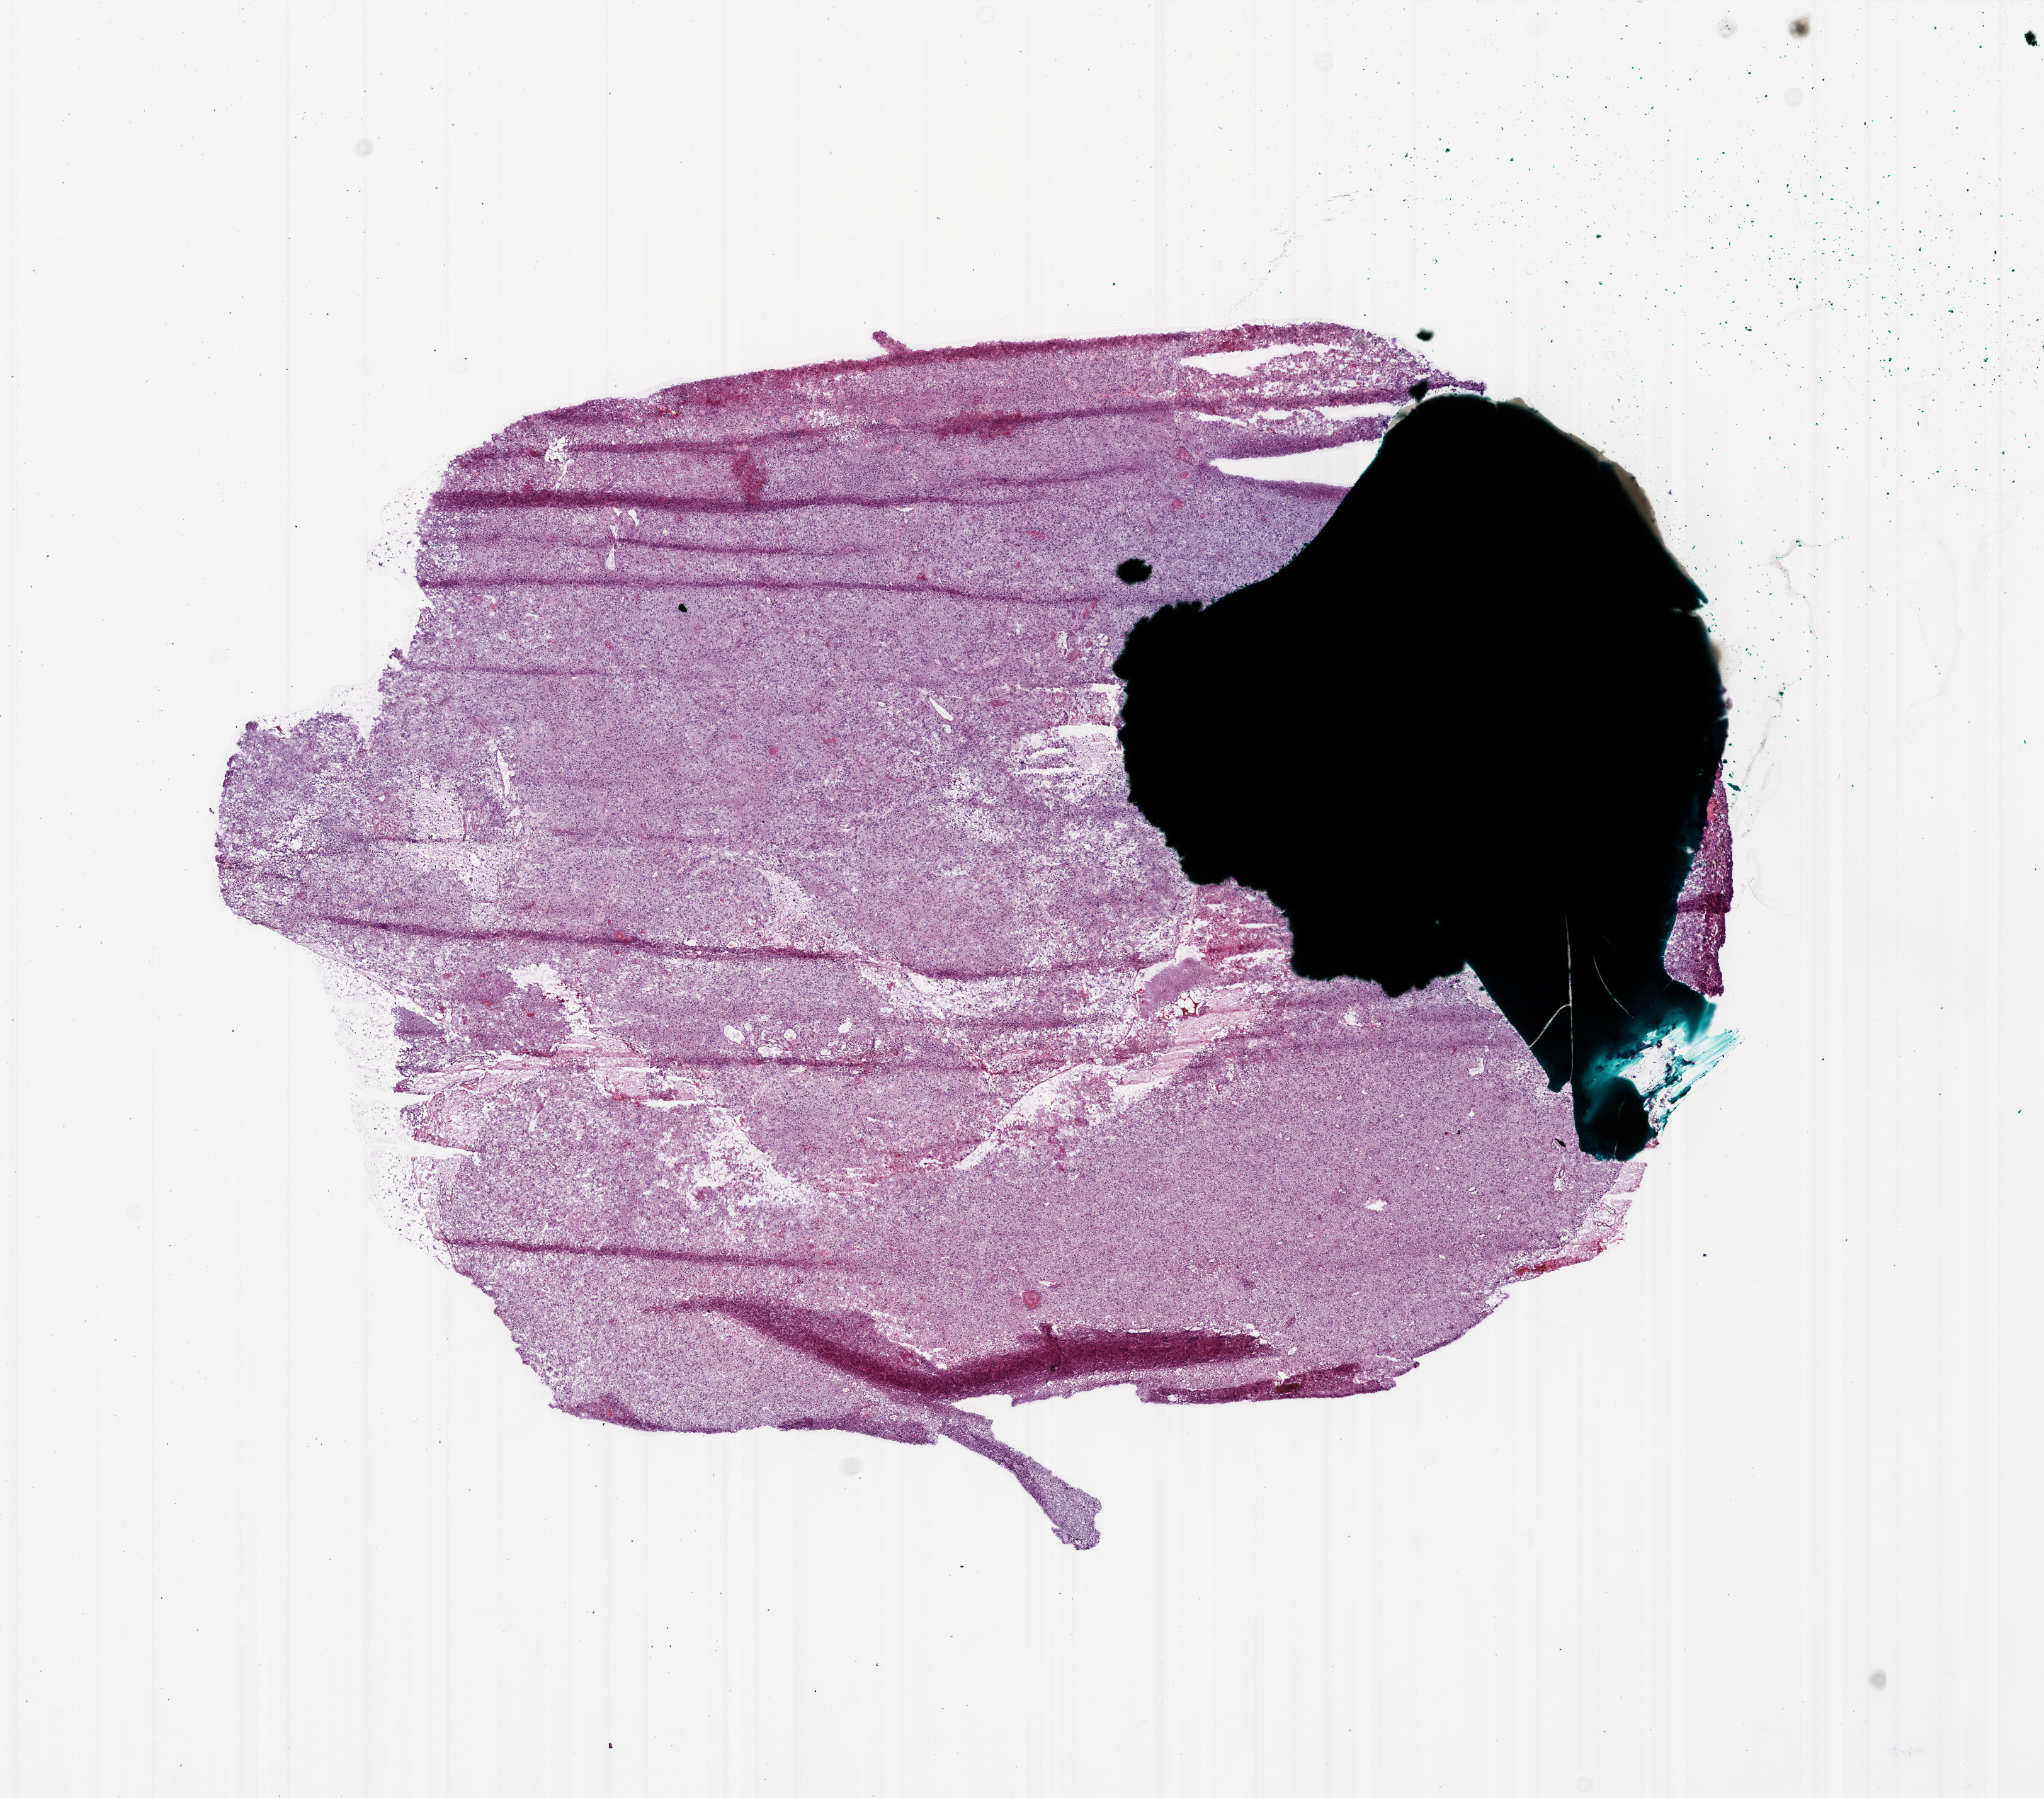
H&E whole-slide image — a low-resolution overview of the entire scanned area, about 13.0 x 11.4 mm (acquisition: 20x scan), frozen section from the bottom of the tissue portion, sample: primary tumour, brain. Male, age 78 years at initial diagnosis. Pathologist review of this section (percent, as recorded): tumour cells 90%, tumour nuclei 95%.
Diagnosis: Glioblastoma.